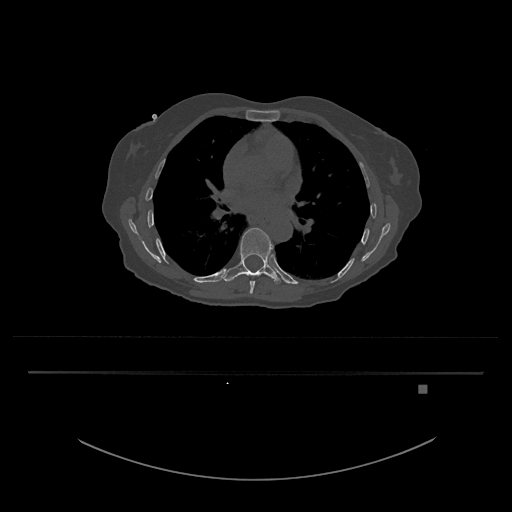
CT including the spine, one axial slice; reconstruction kernel Br40s/3; bone window (W 1800 / L 400 HU); 0.5 mm slice thickness; 512 × 512 image matrix, field of view 500 × 500 mm. Patient: female, 57 years. Case-level facts recorded for this patient, not image findings: primary cancer: cervical.
Structures marked on this image (semi-automatically segmented with operator editing):
- T8 vertebra: bounding box [x1, y1, x2, y2] px = [249, 275, 260, 294]
- T9 vertebra: [223, 228, 281, 284]